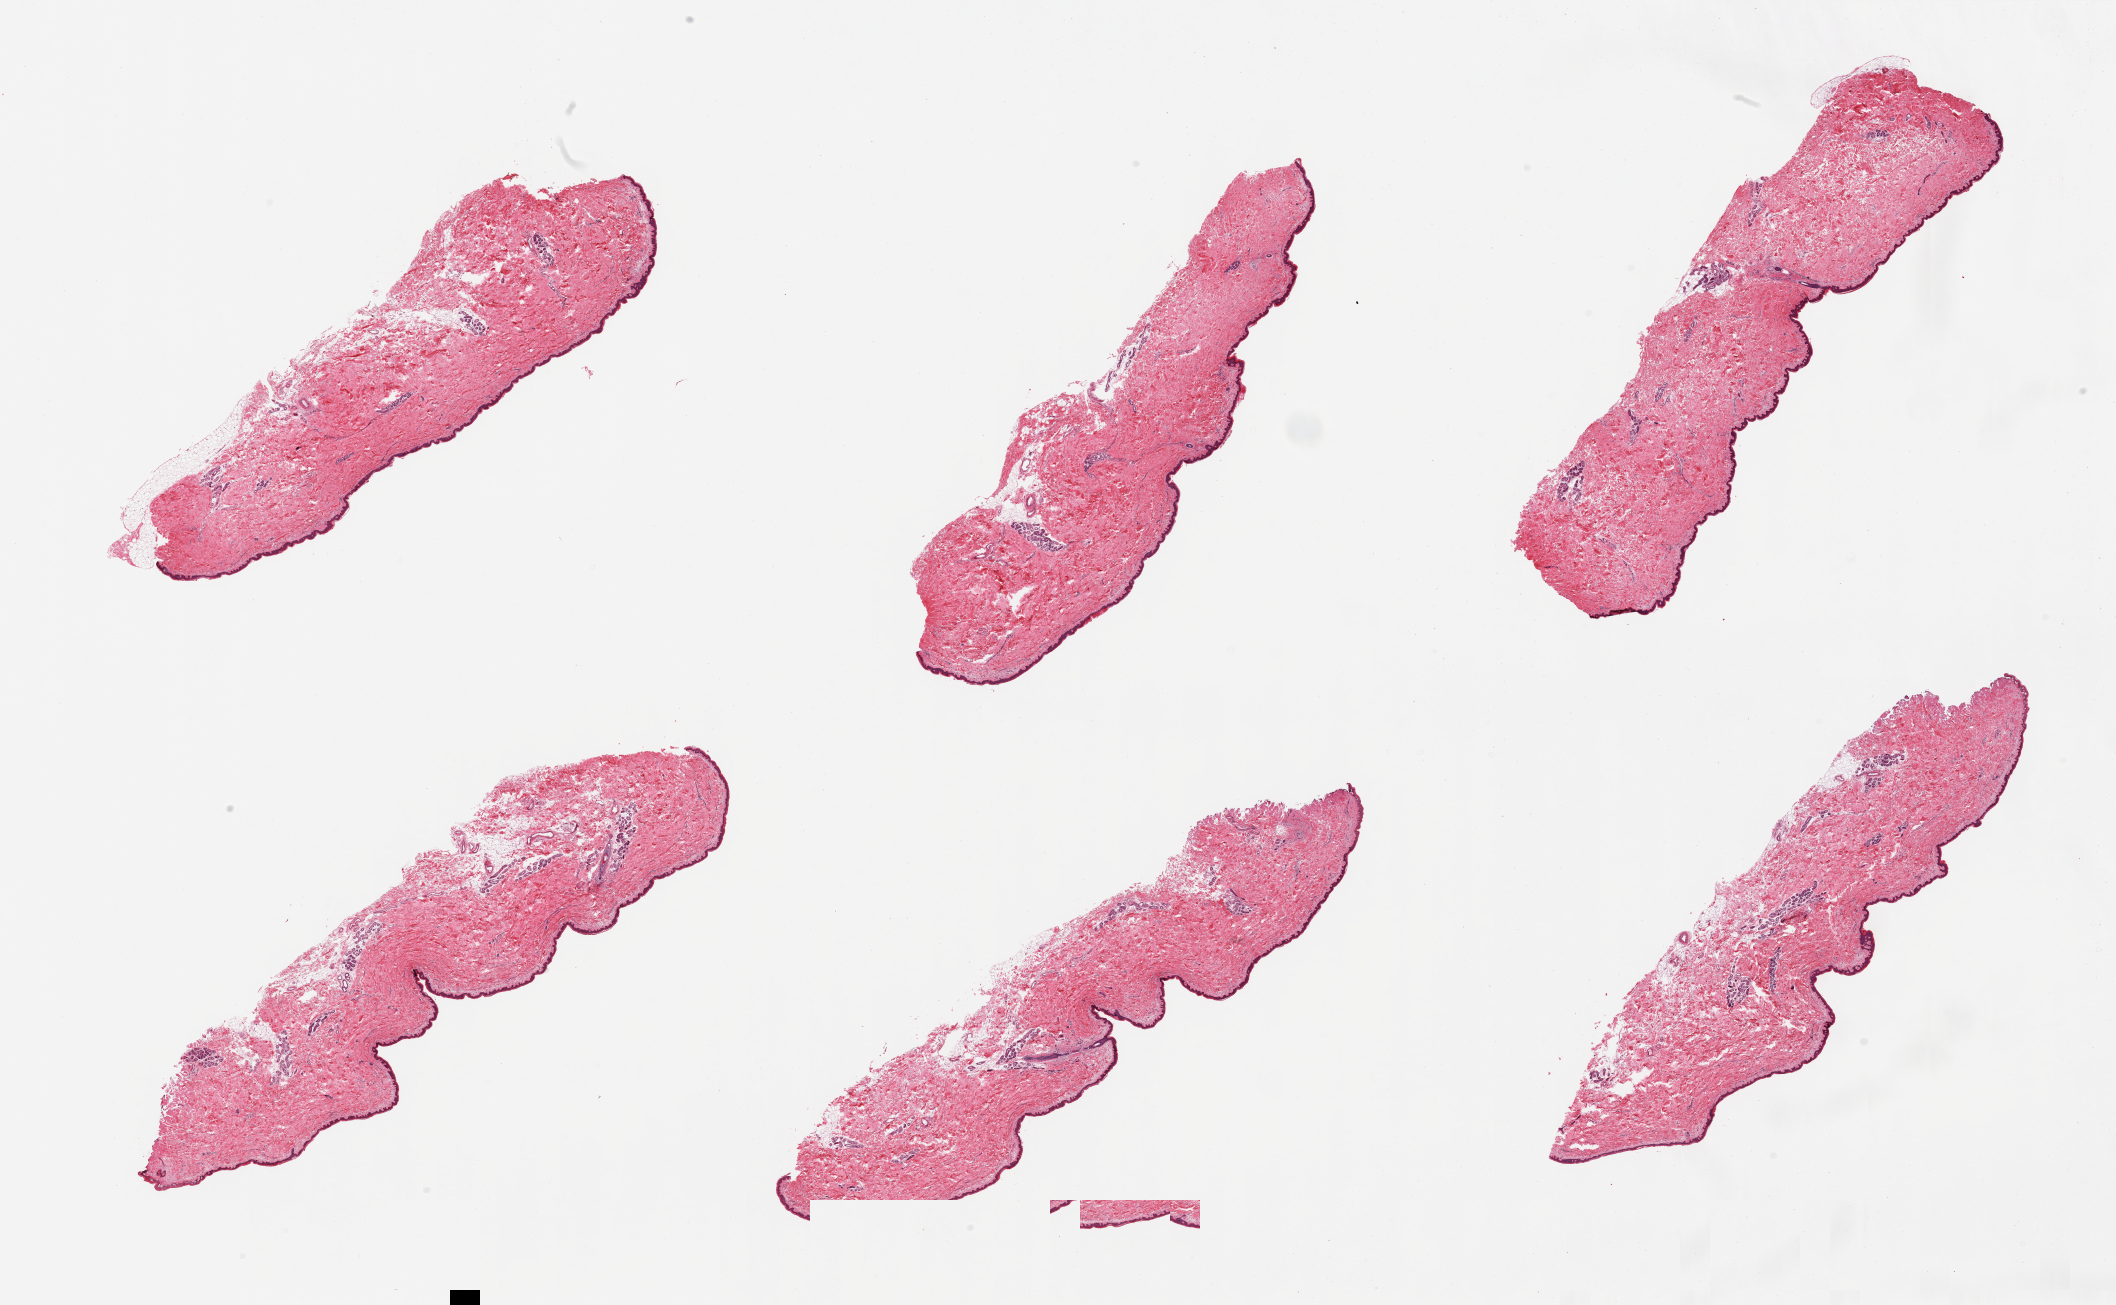
Digitized H&E-stained section, brightfield — a low-resolution overview of the entire scanned area, about 33.5 x 20.6 mm; PAXgene-fixed paraffin-embedded (PFPE) section; section of skin of suprapubic region (target tissue); donor tissue sample. Donor: female.
- review note (as recorded): 6 pieces, predominantly well trimmed with limited attached adipose tissue